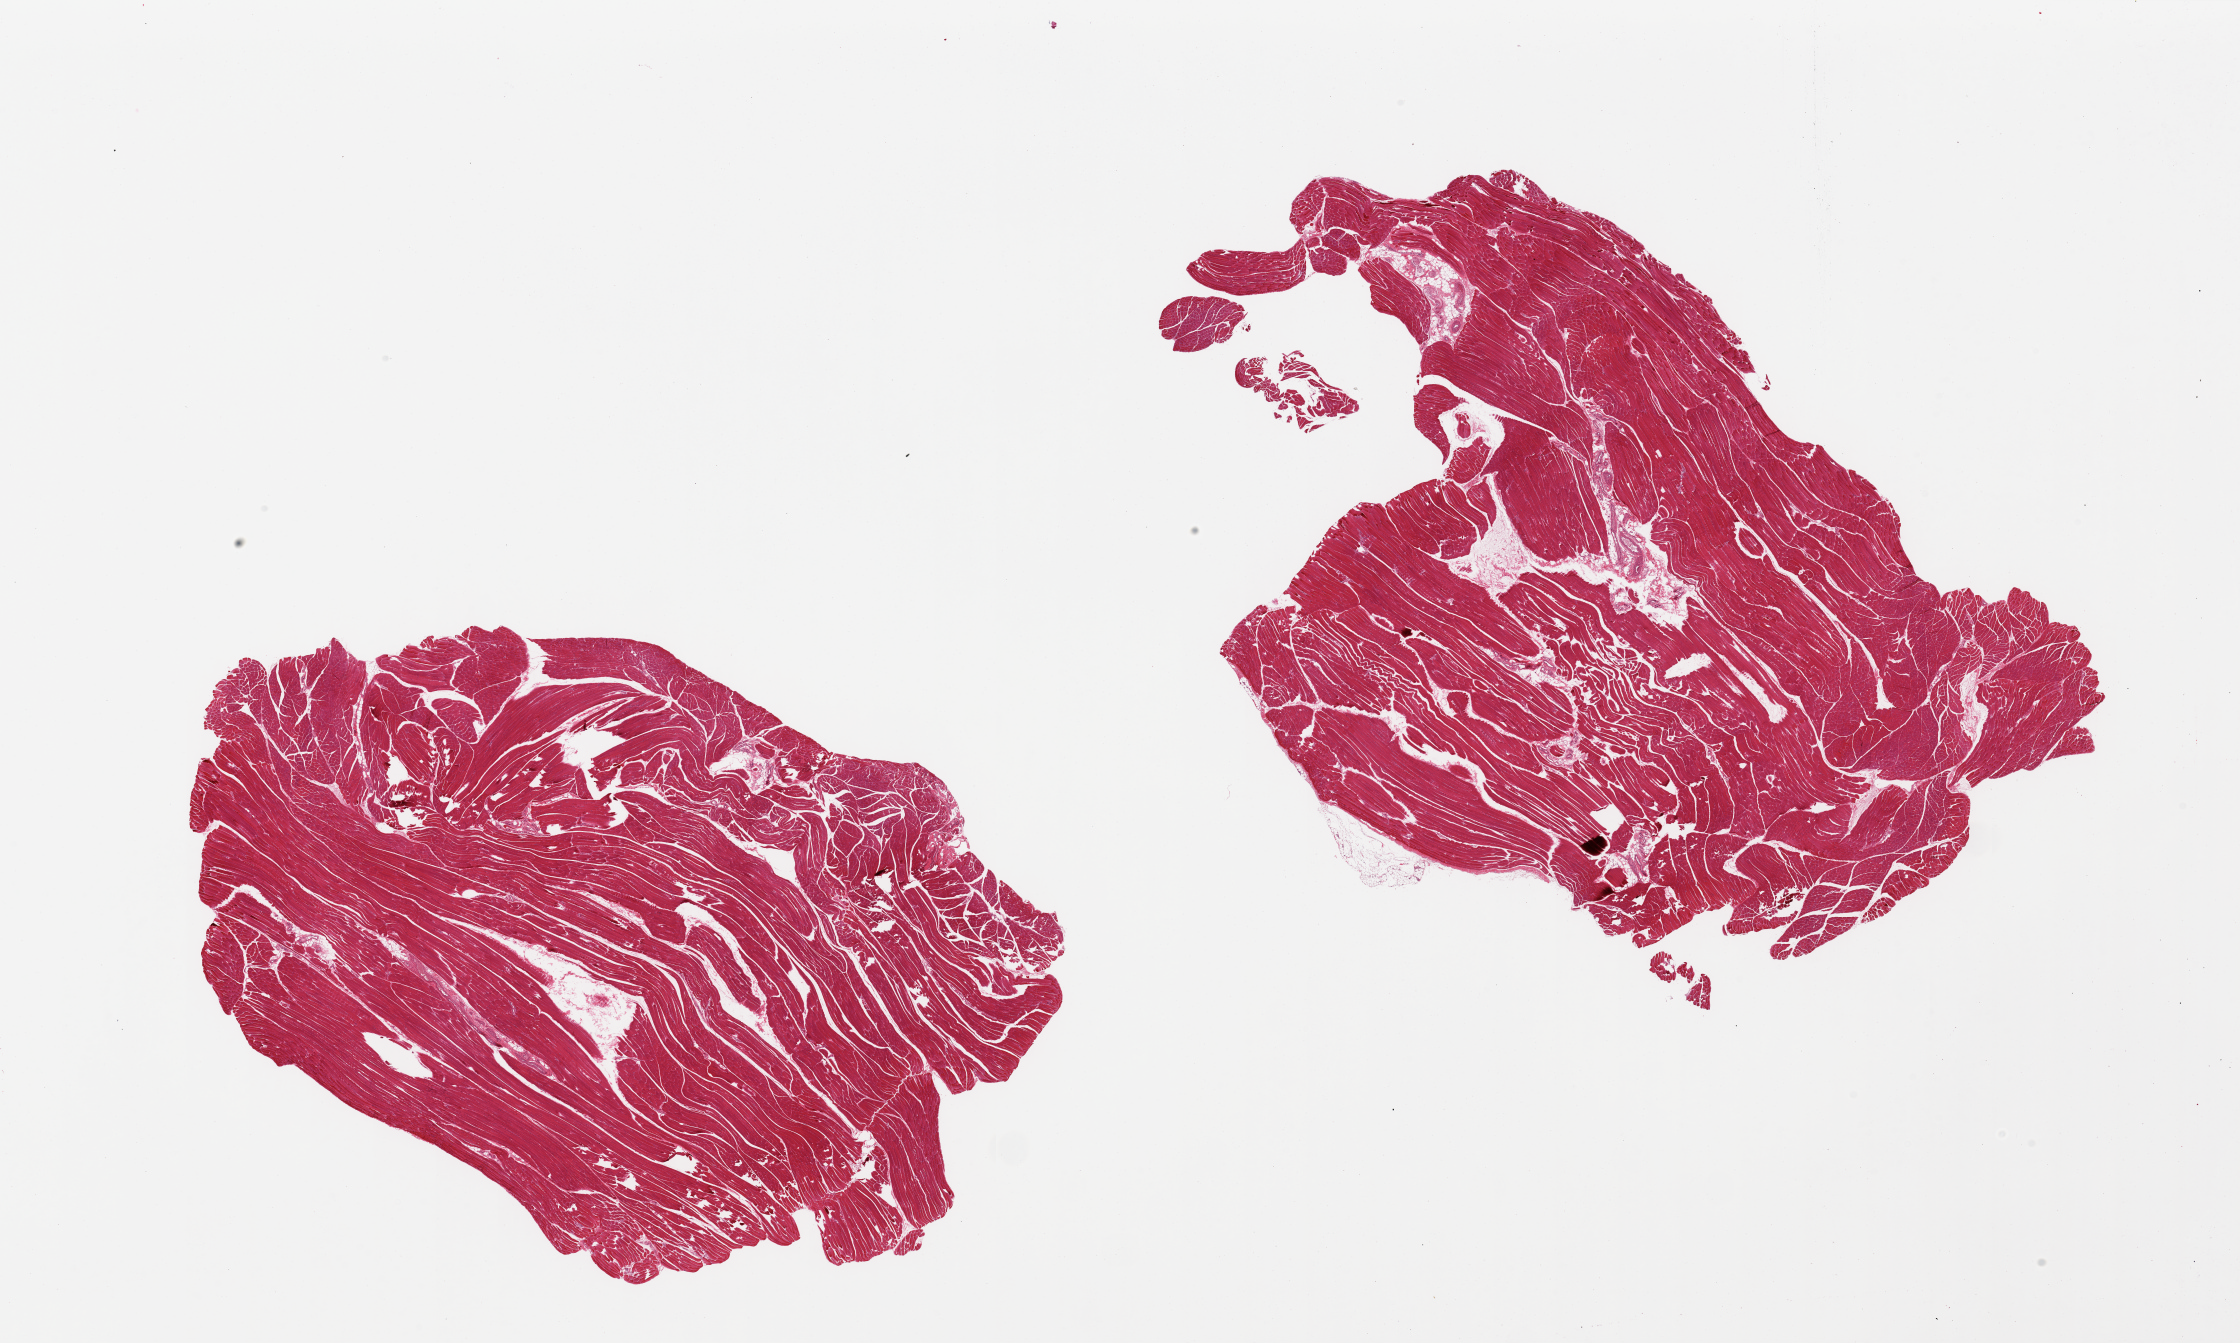
Digitized haematoxylin and eosin-stained section — low-resolution overview of the scanned area, about 35.4 x 21.2 mm (slide scanned at 20x). PAXgene-fixed, paraffin-embedded tissue. Sampled site (target tissue): skeletal muscle. Donor tissue sample.
Pathologist's review note for this sample: 2 pieces, <10% internal adipose tissue.